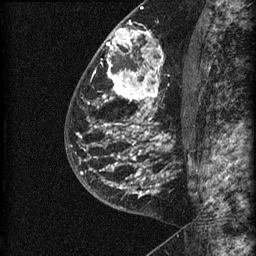
Breast MRI (dynamic contrast-enhanced), one sagittal slice; position 36 of 60 along the scan axis; dynamic contrast-enhanced series, image 2 of 3 at this slice position (ordered by acquisition); 1.5 T; TE 4.2 ms, TR 22.7 ms; 256 × 256 image matrix, field of view 180 × 180 mm. Female patient, age 48 years. Case-level facts recorded for this patient, not image findings: setting: breast cancer imaged before/during neoadjuvant chemotherapy; receptor status: triple-negative.
Outlined on this slice (semi-automatic segmentation, software-assisted and operator-edited):
- analysis volume of interest (the breast-tissue region the enhancement analysis was run in; not a lesion): bounding box (x1, y1, x2, y2) in pixels: (81, 23, 186, 202)
- tumour enhancement mask (voxels above the 90 % enhancement threshold inside the analysis volume of interest): (81, 28, 165, 196)